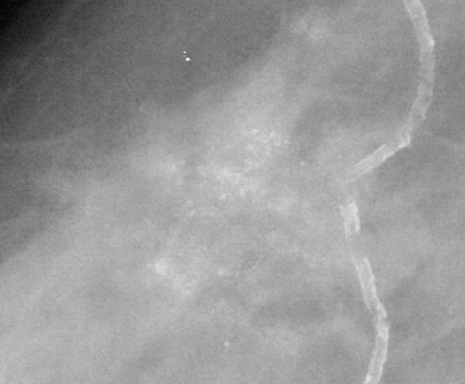
Crop from a digitized film mammogram around one marked abnormality; right breast; CC view; BI-RADS breast density category 3 (scale 1–4).
Marked abnormality: calcifications, morphology punctate / pleomorphic, distribution clustered; BI-RADS assessment category 4; subtlety rating 3 on a 1 (subtle) to 5 (obvious) scale; pathology (as recorded): malignant.